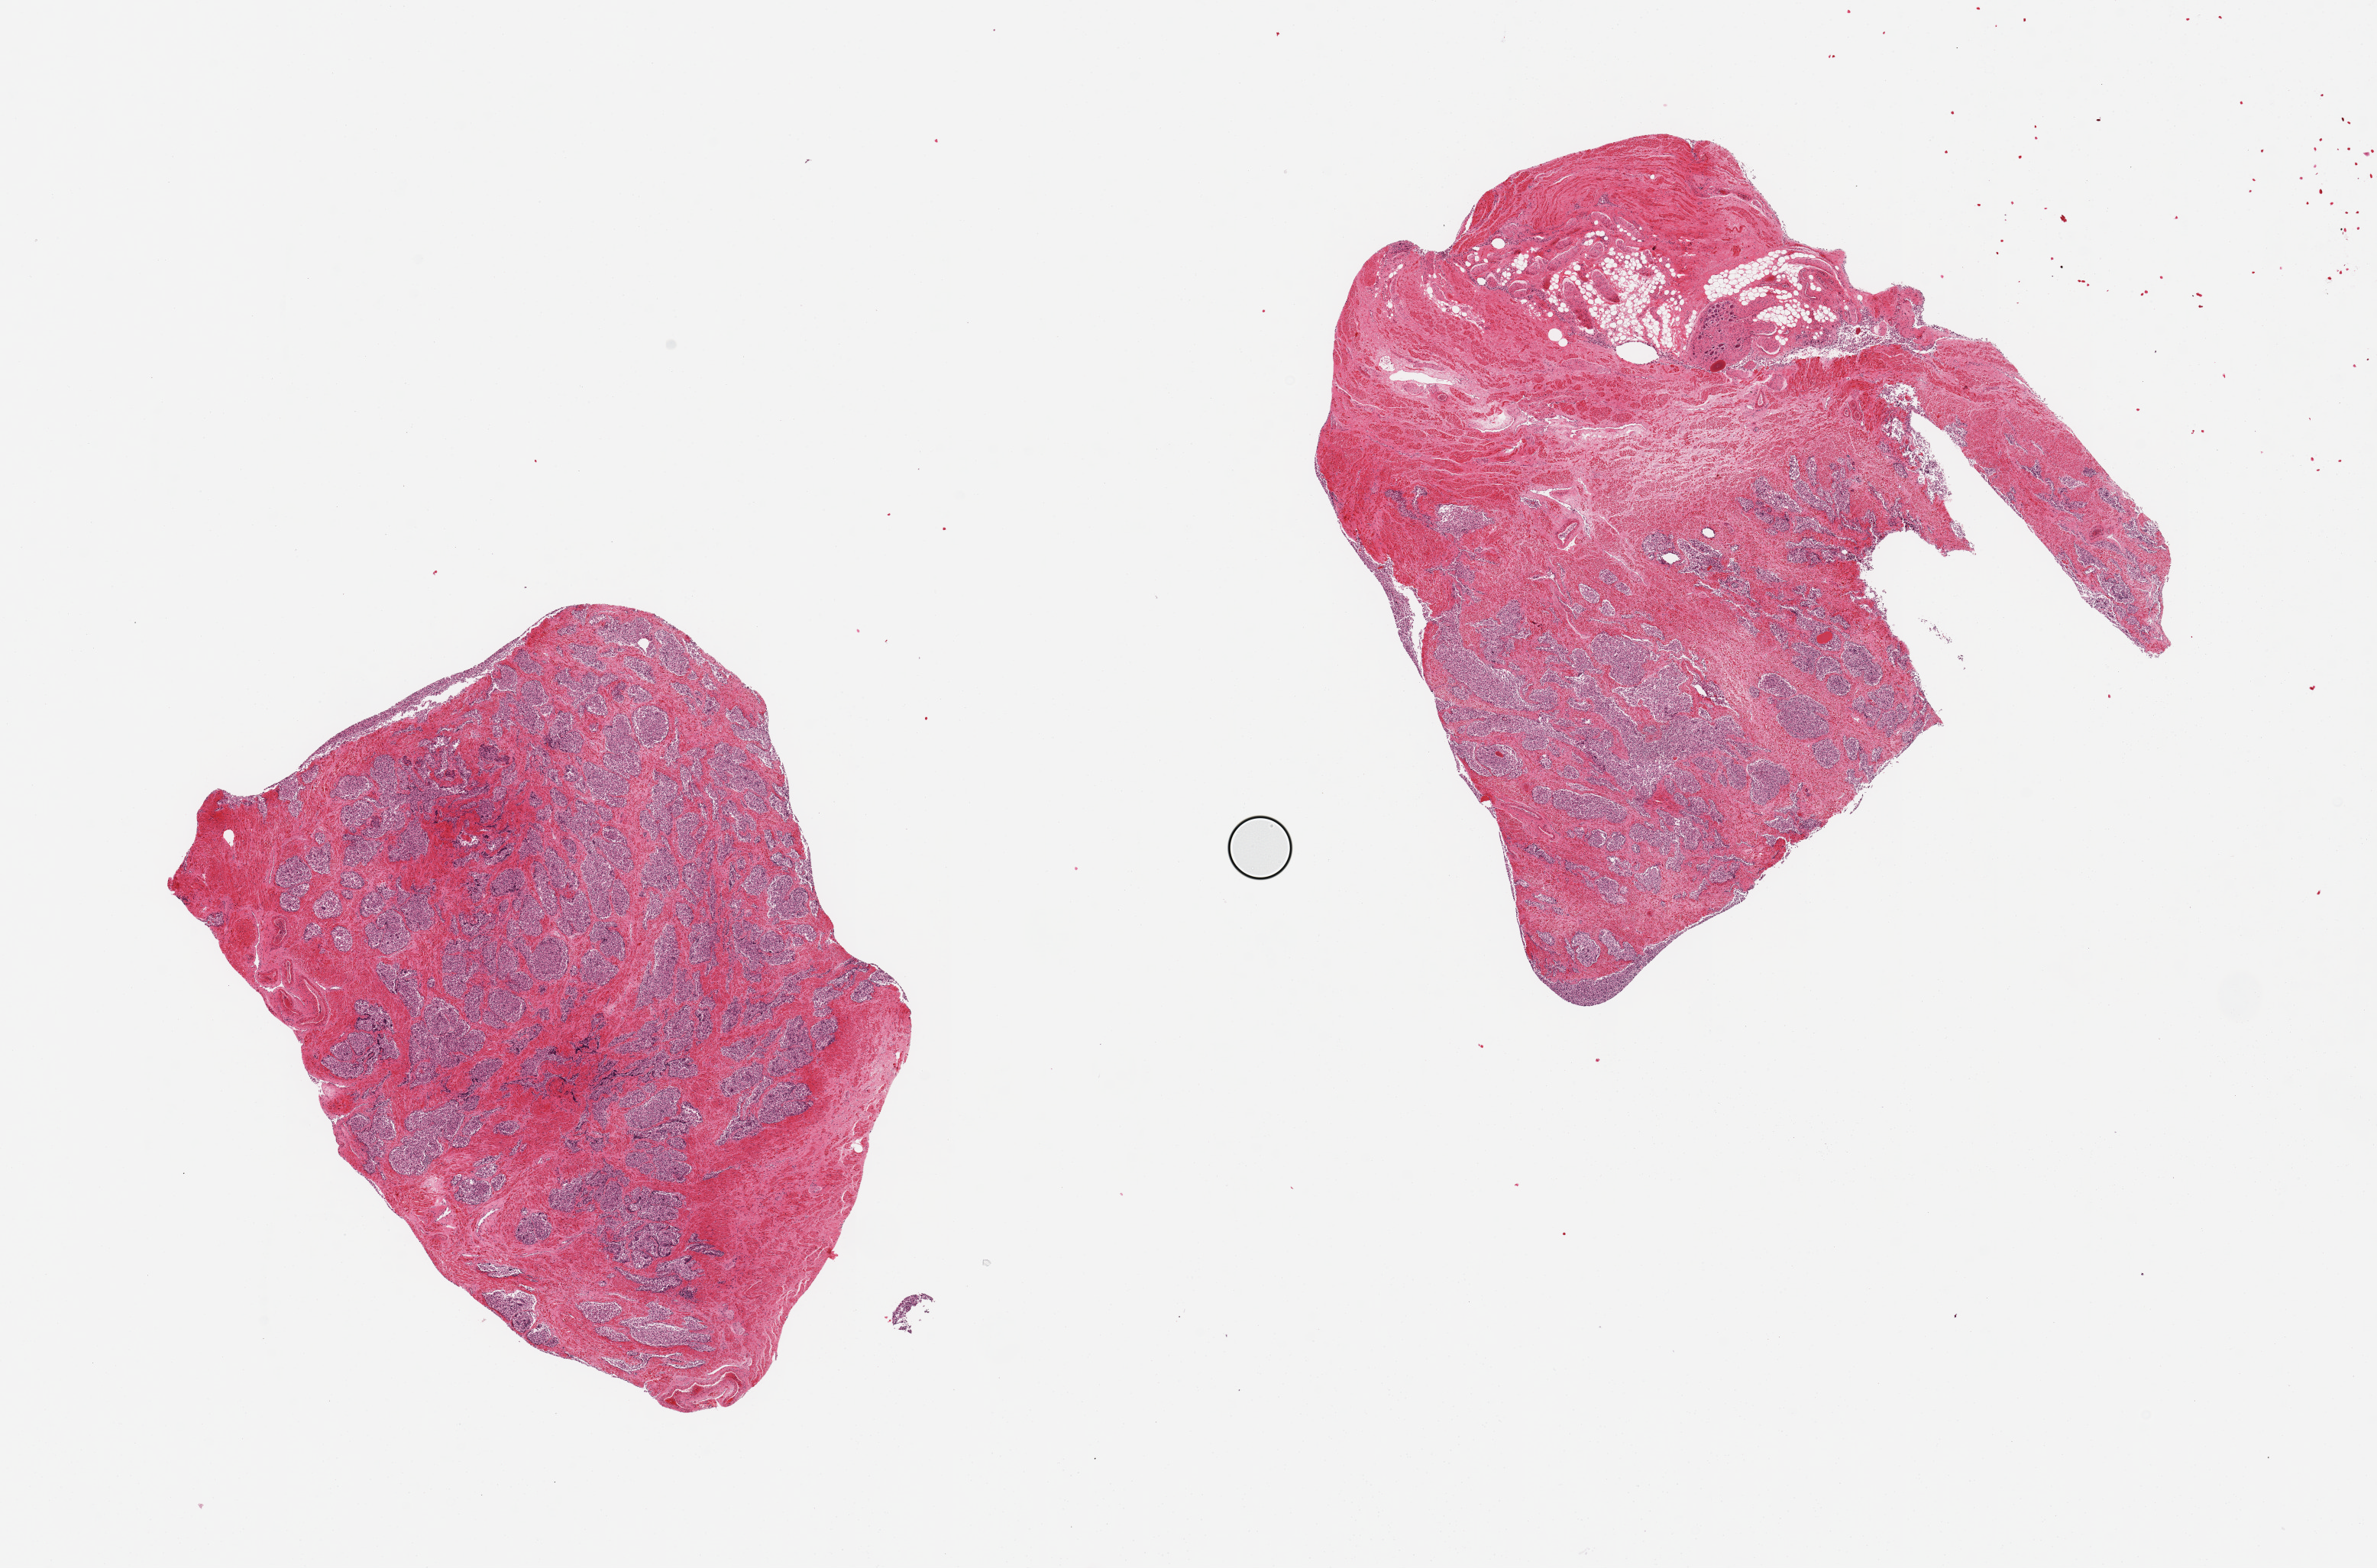
Digitized hematoxylin and eosin (H&E)-stained section — low-resolution overview of the scanned area, about 24.6 x 16.2 mm, PAXgene-fixed, paraffin-embedded tissue, target tissue: prostate, tissue donor sample. Donor sex: male.
Pathologist's review note for this sample: 2 pieces; glands completely autolyzed; stroma intact; collection of ganglion cells.